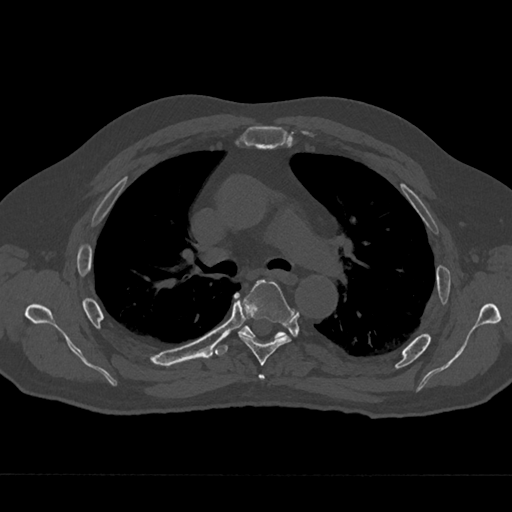
CT including the spine, one axial slice; position 458 of 797 along the scan axis; 120 kVp; bone window (W 1800 / L 400 HU); 0.5 mm slice thickness; 512 × 512 image matrix, field of view 377 × 377 mm. Patient: male, 75 years. From the clinical record (not read from this slice): primary cancer: renal; vertebrae with lytic lesions (as recorded): T4.
Structures marked on this image (semi-automatic segmentation, software-assisted and operator-edited):
- T4 vertebra: bounding box <258,374,265,381> (left, top, right, bottom; pixels)
- T5 vertebra: <238,280,293,366>
- T6 vertebra: <216,326,286,356>